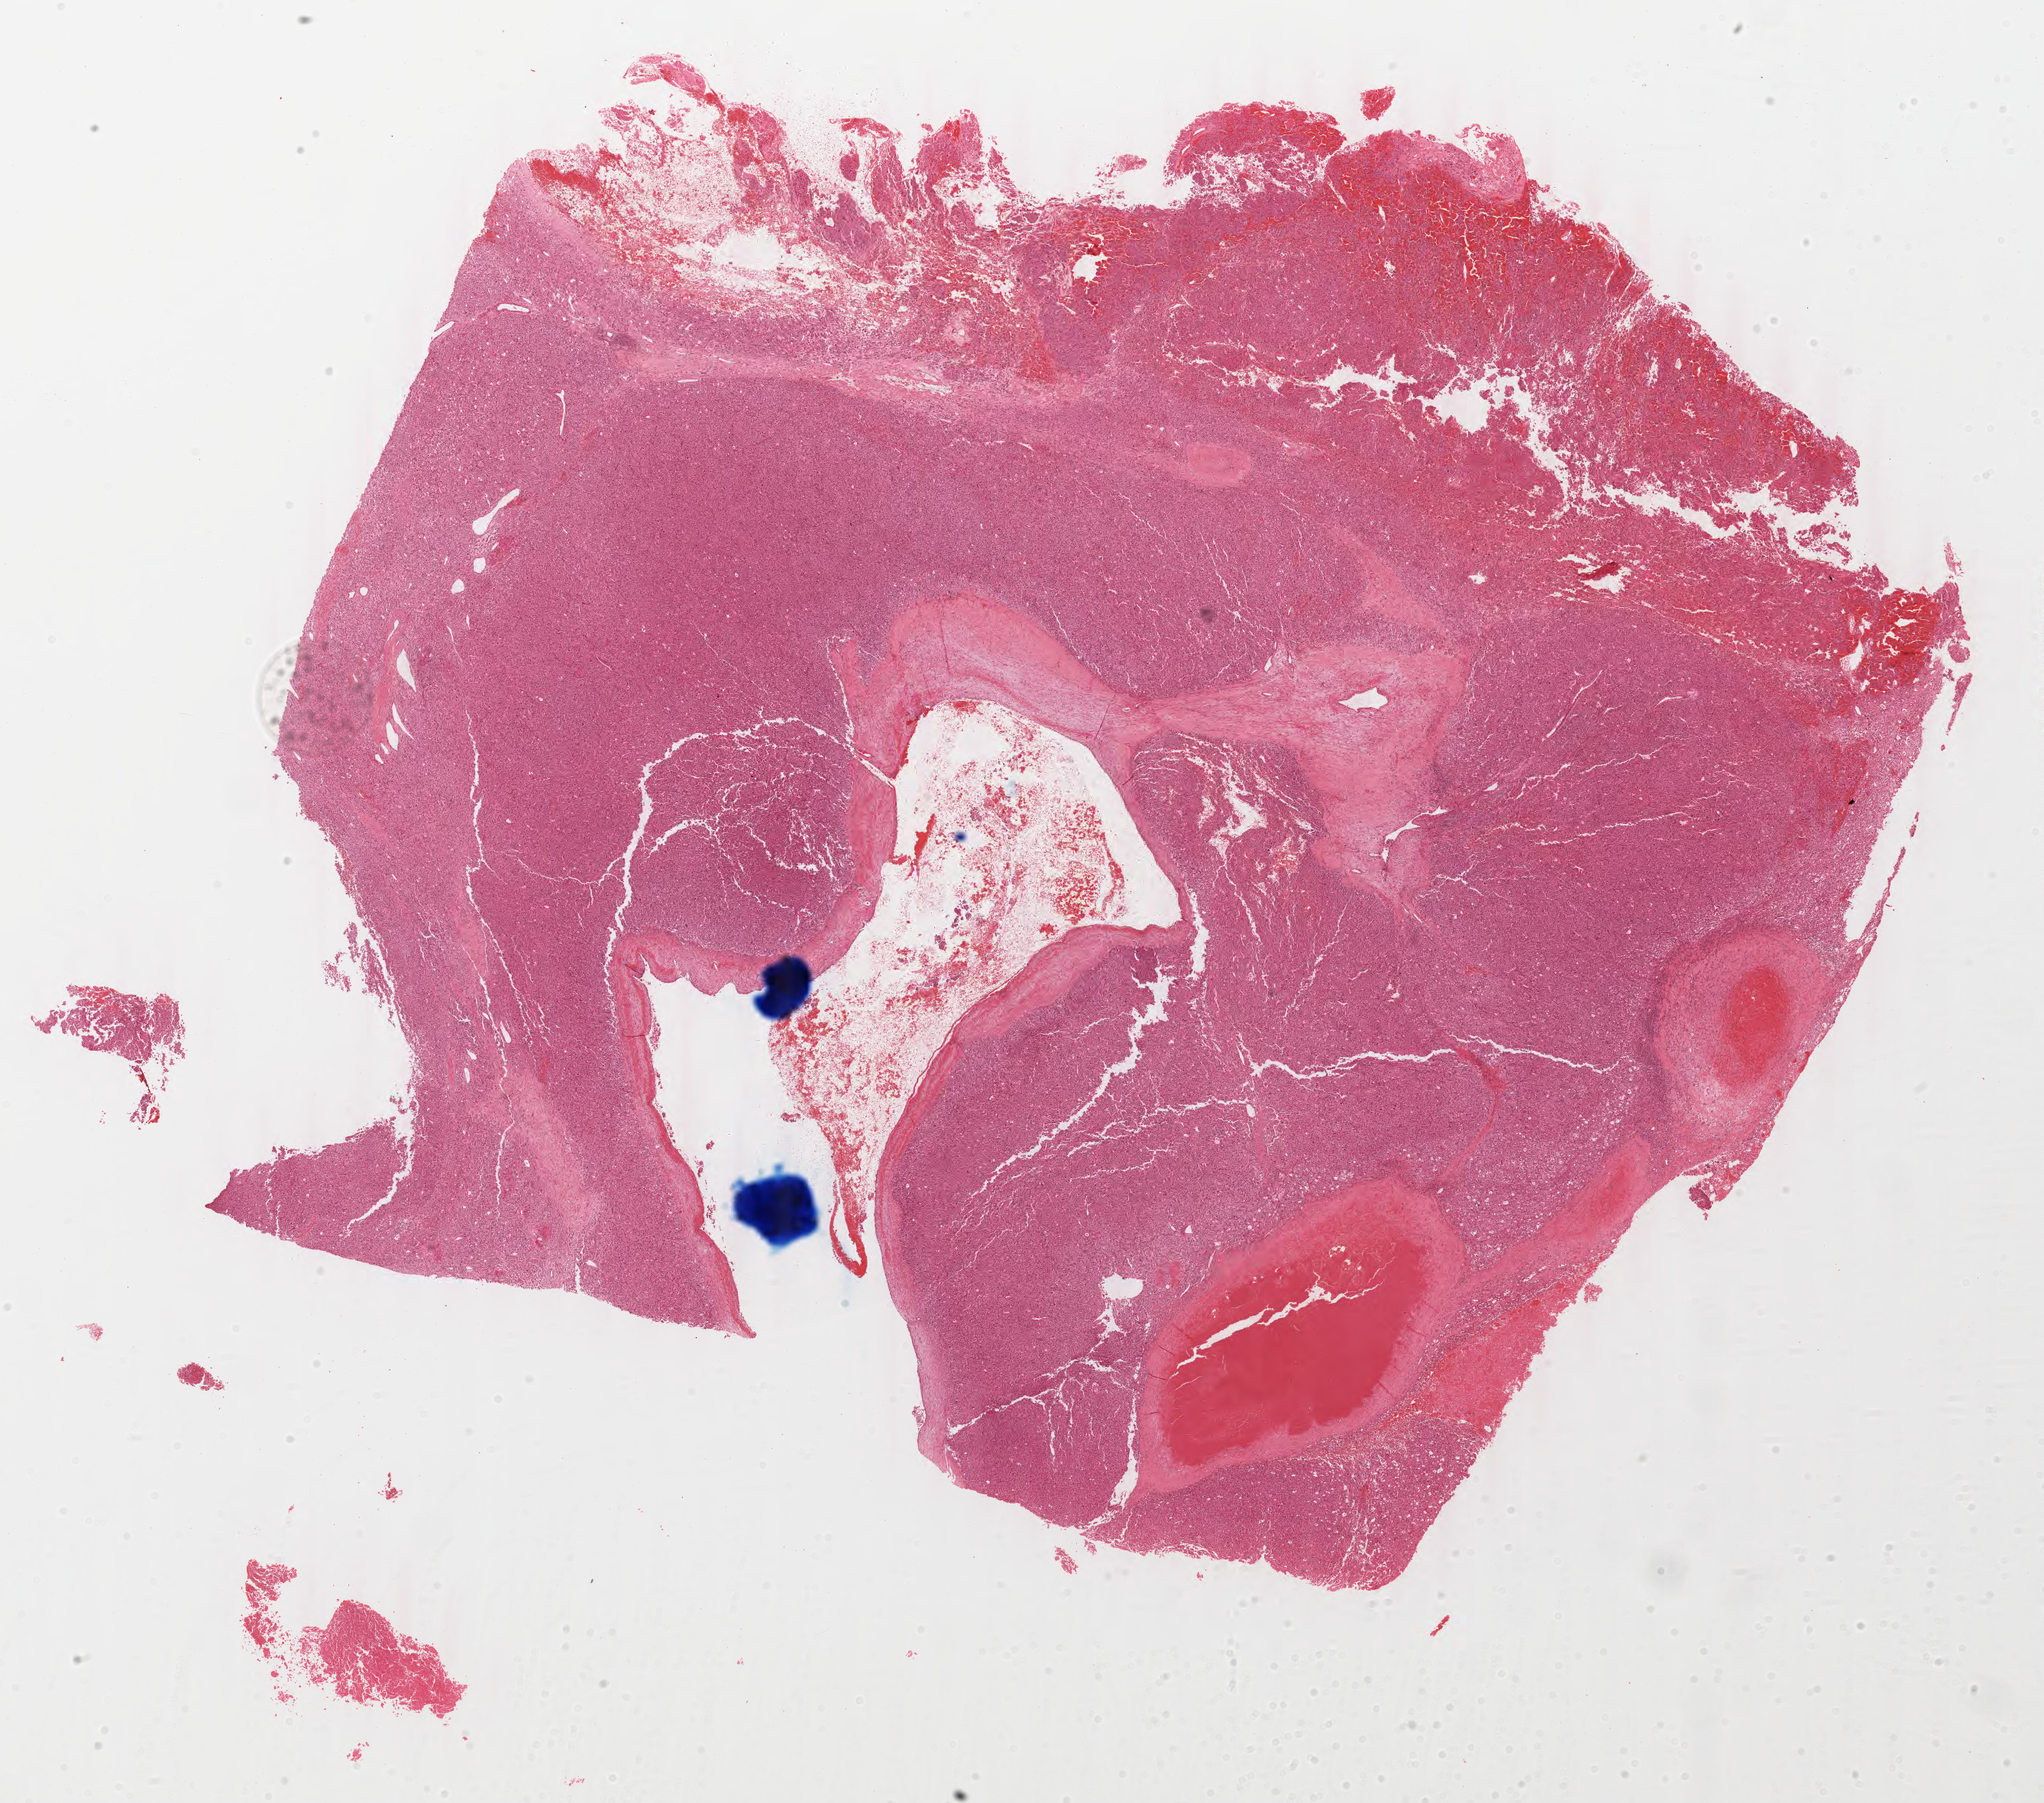
Whole-slide histology image, H&E-stained — a low-resolution overview of the entire scanned area, about 21.1 x 18.7 mm (slide scanned at 40x). Formalin-fixed paraffin-embedded (FFPE) diagnostic section. Primary tumour sample from the adrenal cortex. Male, age 63 years at initial diagnosis.
Histologic diagnosis: Adrenal cortical carcinoma (cortex of adrenal gland). Laterality: left.